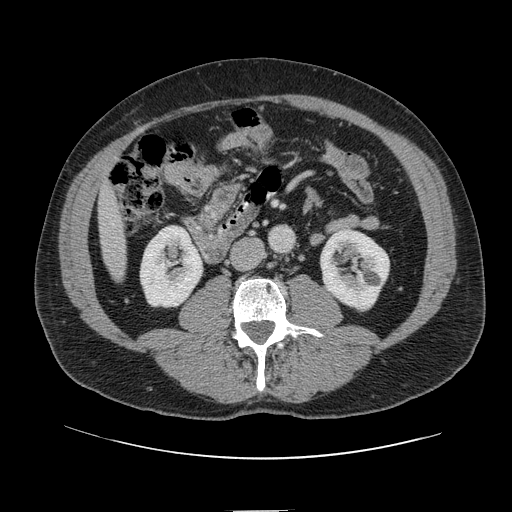
Contrast-enhanced abdominal CT, one axial slice; slice 15 of 161 in the series (ordered by position); 120 kVp; intravenous contrast given; soft-tissue window (W 400 / L 40 HU); 2.5 mm slice thickness; 512 × 512 image matrix, field of view 412 × 412 mm. Male patient, age 66 years. From the clinical record (not read from this slice): diagnosis: colorectal cancer liver metastases, imaged before liver resection; multiple liver metastases: no; largest metastasis: 3.5 cm; disease in both lobes: no.
Annotated regions visible in this slice (outlined manually by an expert reader):
- liver: bounding box <100,188,126,280> (left, top, right, bottom; pixels)
- planned liver remnant (the part of the liver to remain after resection): <100,187,121,244>